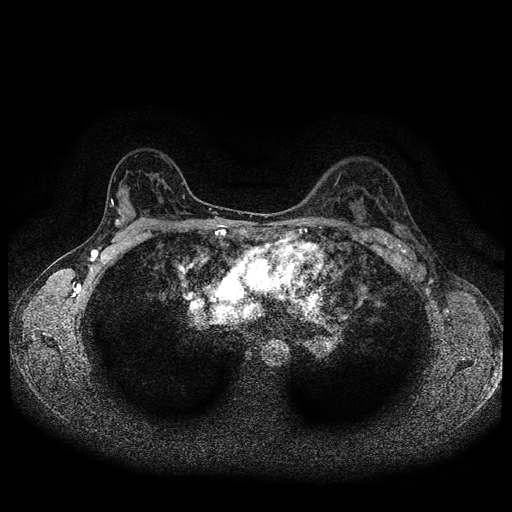
Breast MRI (dynamic contrast-enhanced, multi-phase), one axial slice. Position 68 of 116 along the scan axis. Dynamic contrast-enhanced series, time point 2 of 5 at this slice position (early post-contrast). 1.5 T. TE 2.7 ms, TR 5.4 ms. 2 mm slice thickness. 512 × 512 image matrix, field of view 330 × 330 mm. Female patient, age 36 years.
Annotated regions visible in this slice (semi-automatically segmented with operator editing):
- breast lesion (labelled 'tumour' in the annotation; benign lesions carry a separate 'benign' label): bounding box (x1, y1, x2, y2) in pixels: (114, 218, 123, 226)